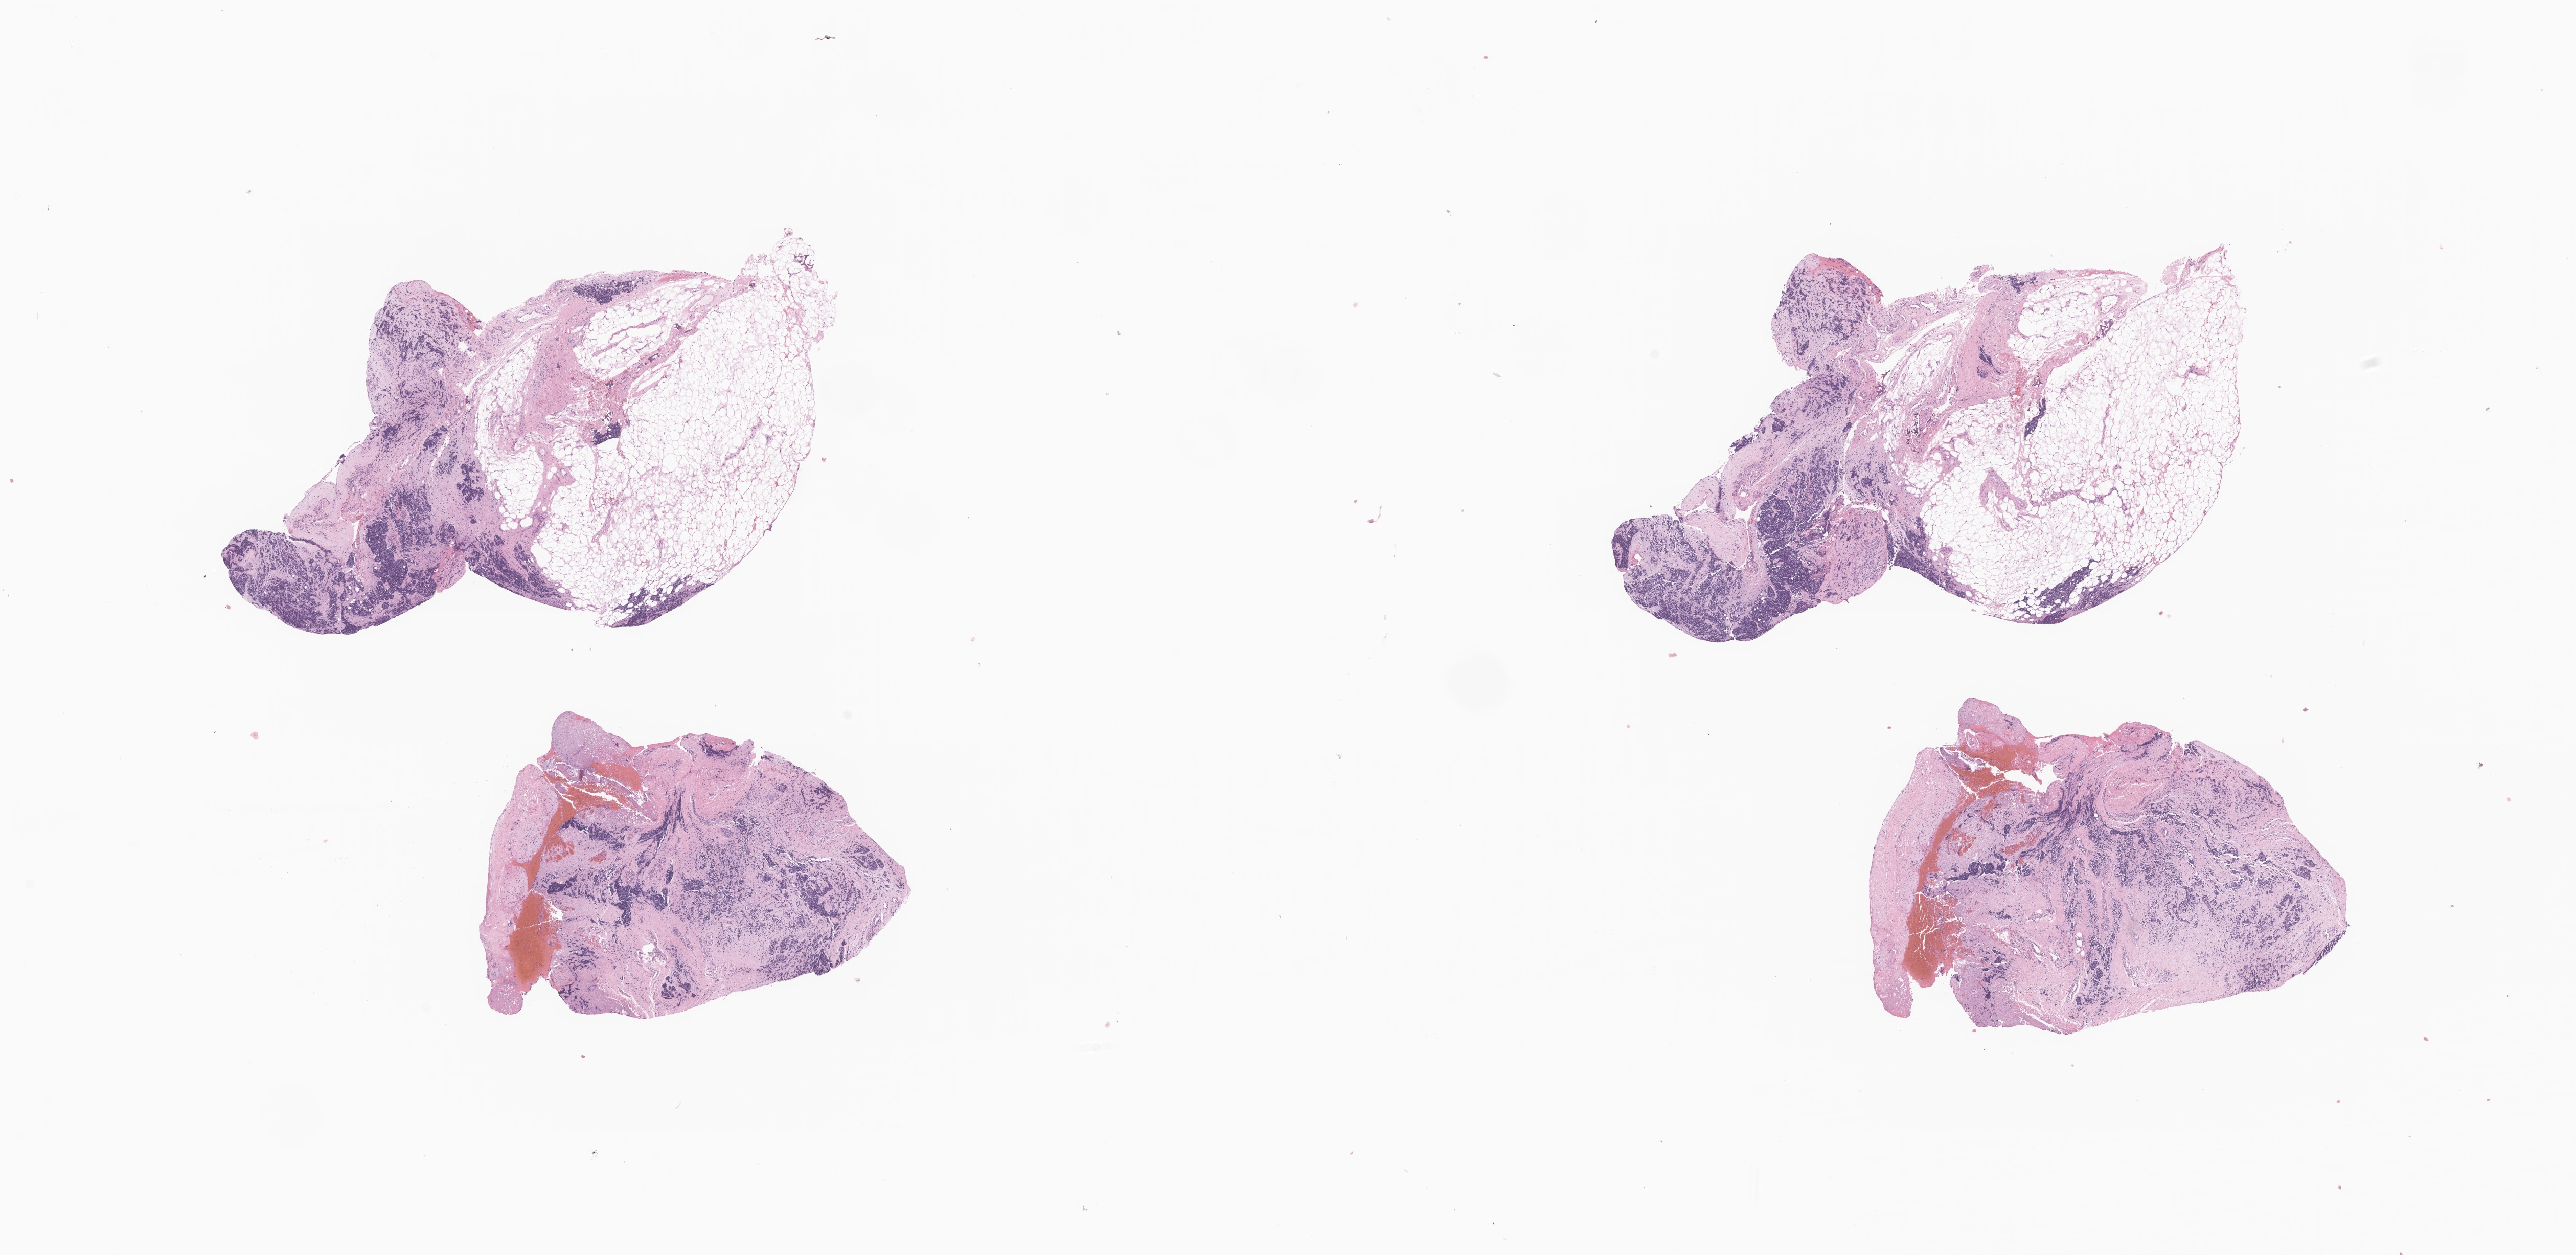
Digitized H&E-stained section of tumor tissue from the head and neck — whole scanned area (about 21.2 x 10.3 mm) shown as a low-resolution overview, formalin-fixed paraffin-embedded section. Patient: male, age 193 days.
Tissue or organ of origin (case record): head, face or neck. Diagnosis (ICD-O-3 morphology term): Rhabdomyosarcoma, NOS.